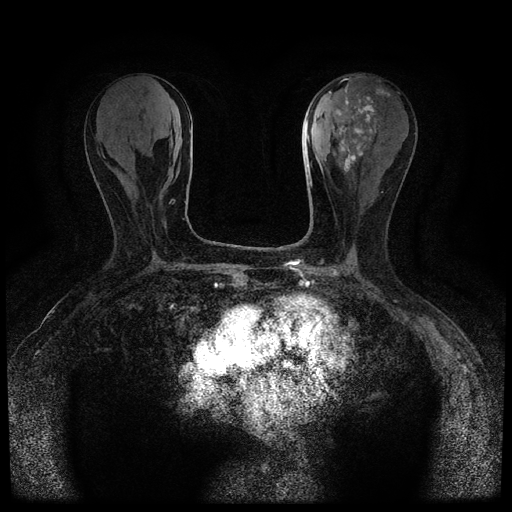
Breast MRI (dynamic contrast-enhanced, multi-phase), one axial slice. Slice 36 of 116 in the series (ordered by position). Dynamic contrast-enhanced series, time point 2 of 5 at this slice position (early post-contrast). 1.5 T. TE 2.7 ms, TR 5.4 ms. 2 mm slice thickness. 512 × 512 image matrix. Female patient, age 80 years.
Structures marked on this image (semi-automatically segmented with operator editing):
- breast lesion (labelled 'tumour' in the annotation; benign lesions carry a separate 'benign' label): box from (x=334, y=87) to (x=390, y=172) px